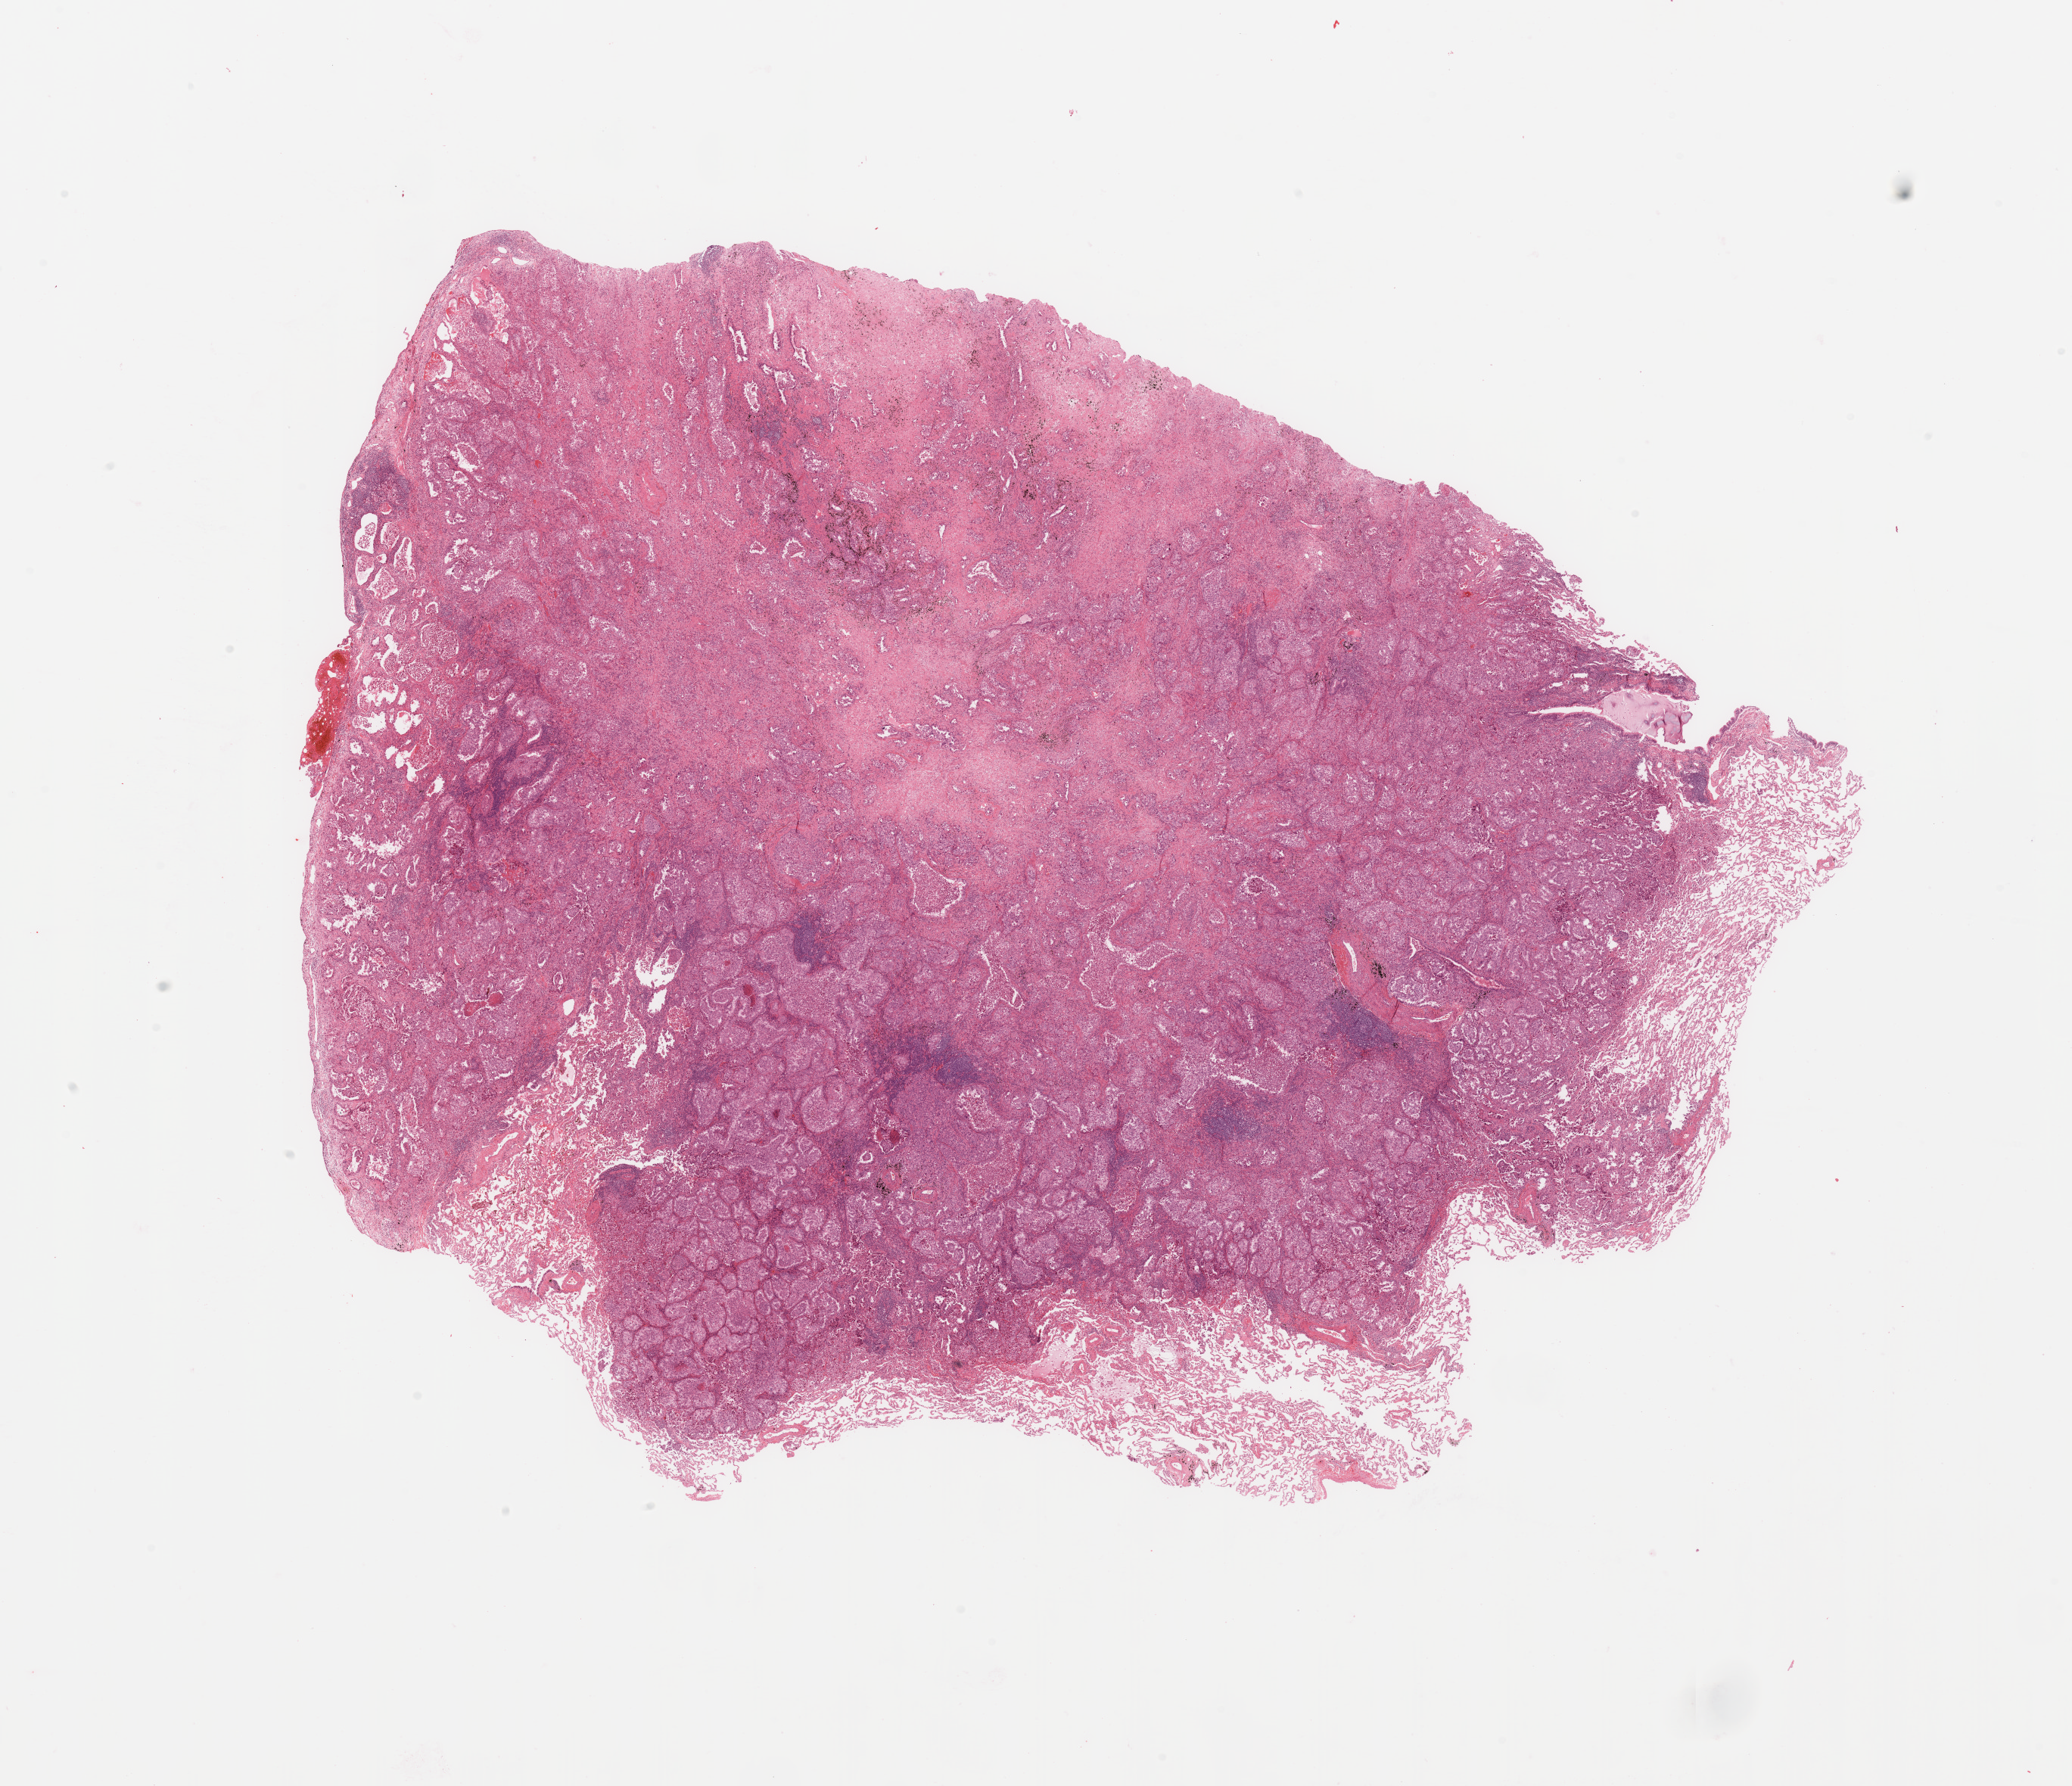
Hematoxylin and eosin (H&E) stained whole-slide image — whole scanned area (about 21.7 x 18.7 mm) shown as a low-resolution overview. Lung, tumour tissue. 62-year-old female patient. Histologic grade: G3 (poorly differentiated).
* AJCC pathologic stage: IB
* diagnosis: Adenocarcinoma, NOS
* primary tumour site (as recorded): left upper lobe